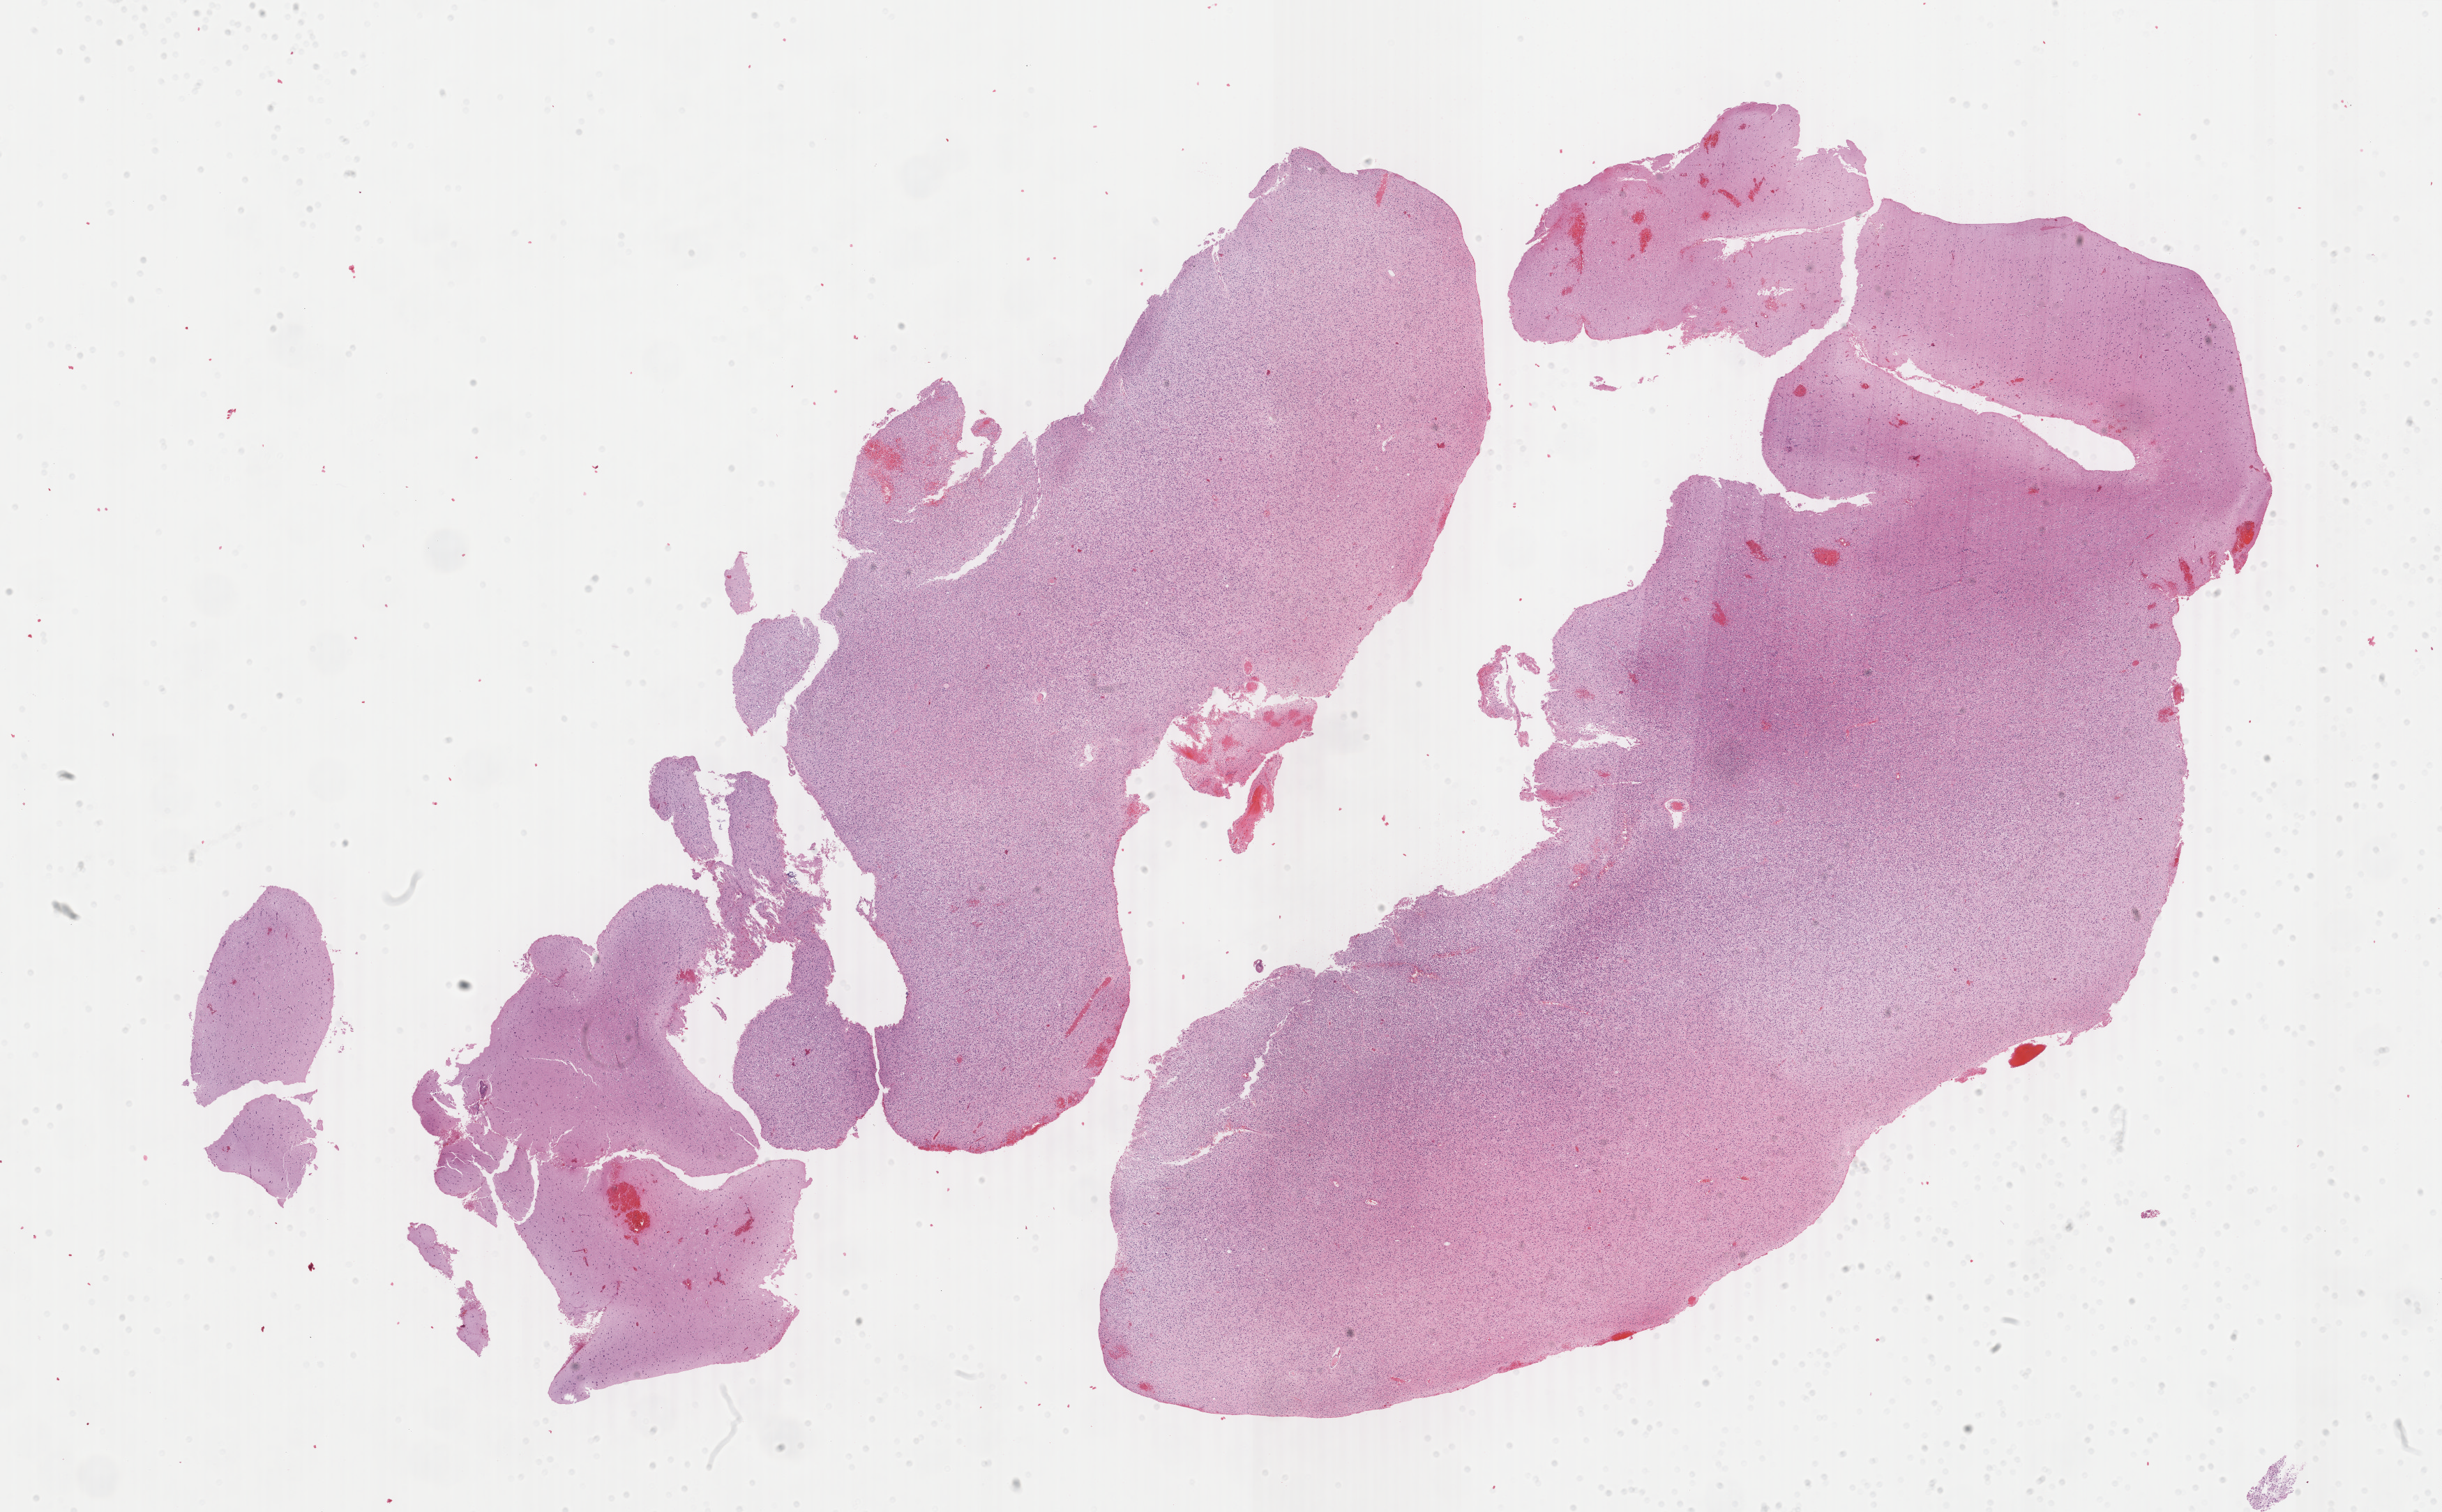
Whole-slide histology image, H&E — shown as a low-resolution overview of the whole scanned area (about 27.8 x 17.2 mm, from a 40x scan), formalin-fixed paraffin-embedded (FFPE) diagnostic section, primary tumour sample from the brain. Male, age 30 years at initial diagnosis. Histologic grade: G3 (poorly differentiated).
Pathologic diagnosis: Mixed glioma (cerebrum).